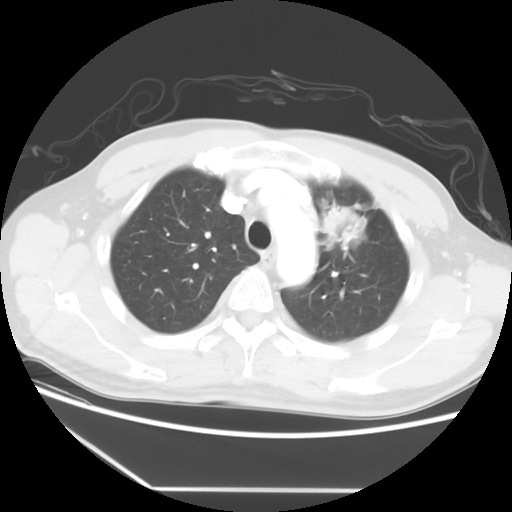
Chest CT, one axial slice; position 42 of 56 along the scan axis; reconstruction kernel STANDARD; lung window (W 1500 / L -600 HU); 5 mm slice thickness; 512 × 512 image matrix, field of view 373 × 373 mm. Patient: male, 53 years. From the clinical record (not read from this slice): clinical TNM (as recorded): T2a N1 M1b.
Annotated regions visible in this slice (bounding box drawn by a radiologist):
- lung tumour (recorded histology: adenocarcinoma): box from (x=323, y=198) to (x=366, y=249) px